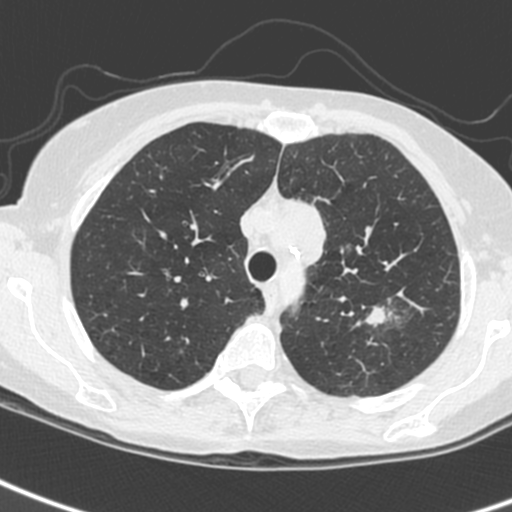
Chest CT (low-dose screening protocol), one axial image; baseline screening round; lung window (W 1500 / L -600 HU); standard (soft-tissue) reconstruction kernel (C); slice 50 of 242 in the series; 512 × 512 image matrix, field of view 284 × 284 mm. Female participant, aged 61 years at enrolment. Current smoker at enrolment.
Lesion marked by an expert reader, bounding box (x1, y1, x2, y2) in pixels: (345, 292, 411, 347). The screening reader recorded 2 non-calcified nodules or masses ≥4 mm on this exam (left upper lobe, left upper lobe); which of them this box marks is not recorded. Participant outcome: lung cancer diagnosed 29 days after this screen — small cell carcinoma, NOS, left upper lobe, stage IV (AJCC 6th edition).